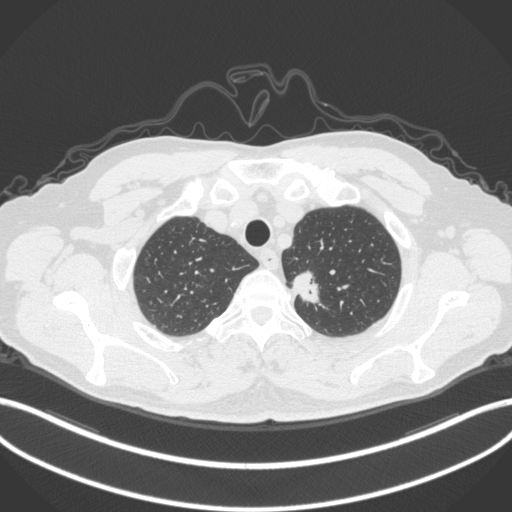
Chest CT, one axial slice; slice 326 of 382 in the series (ordered by position); reconstruction kernel B31f; 120 kVp; lung window (W 1500 / L -600 HU); 512 × 512 image matrix. Male patient, age 64 years. Case-level facts recorded for this patient, not image findings: clinical TNM (as recorded): T1c N0 M0.
Structures marked on this image (rectangle marked by the reading radiologist):
- lung tumour (recorded histology: adenocarcinoma): box from (x=291, y=268) to (x=326, y=311) px